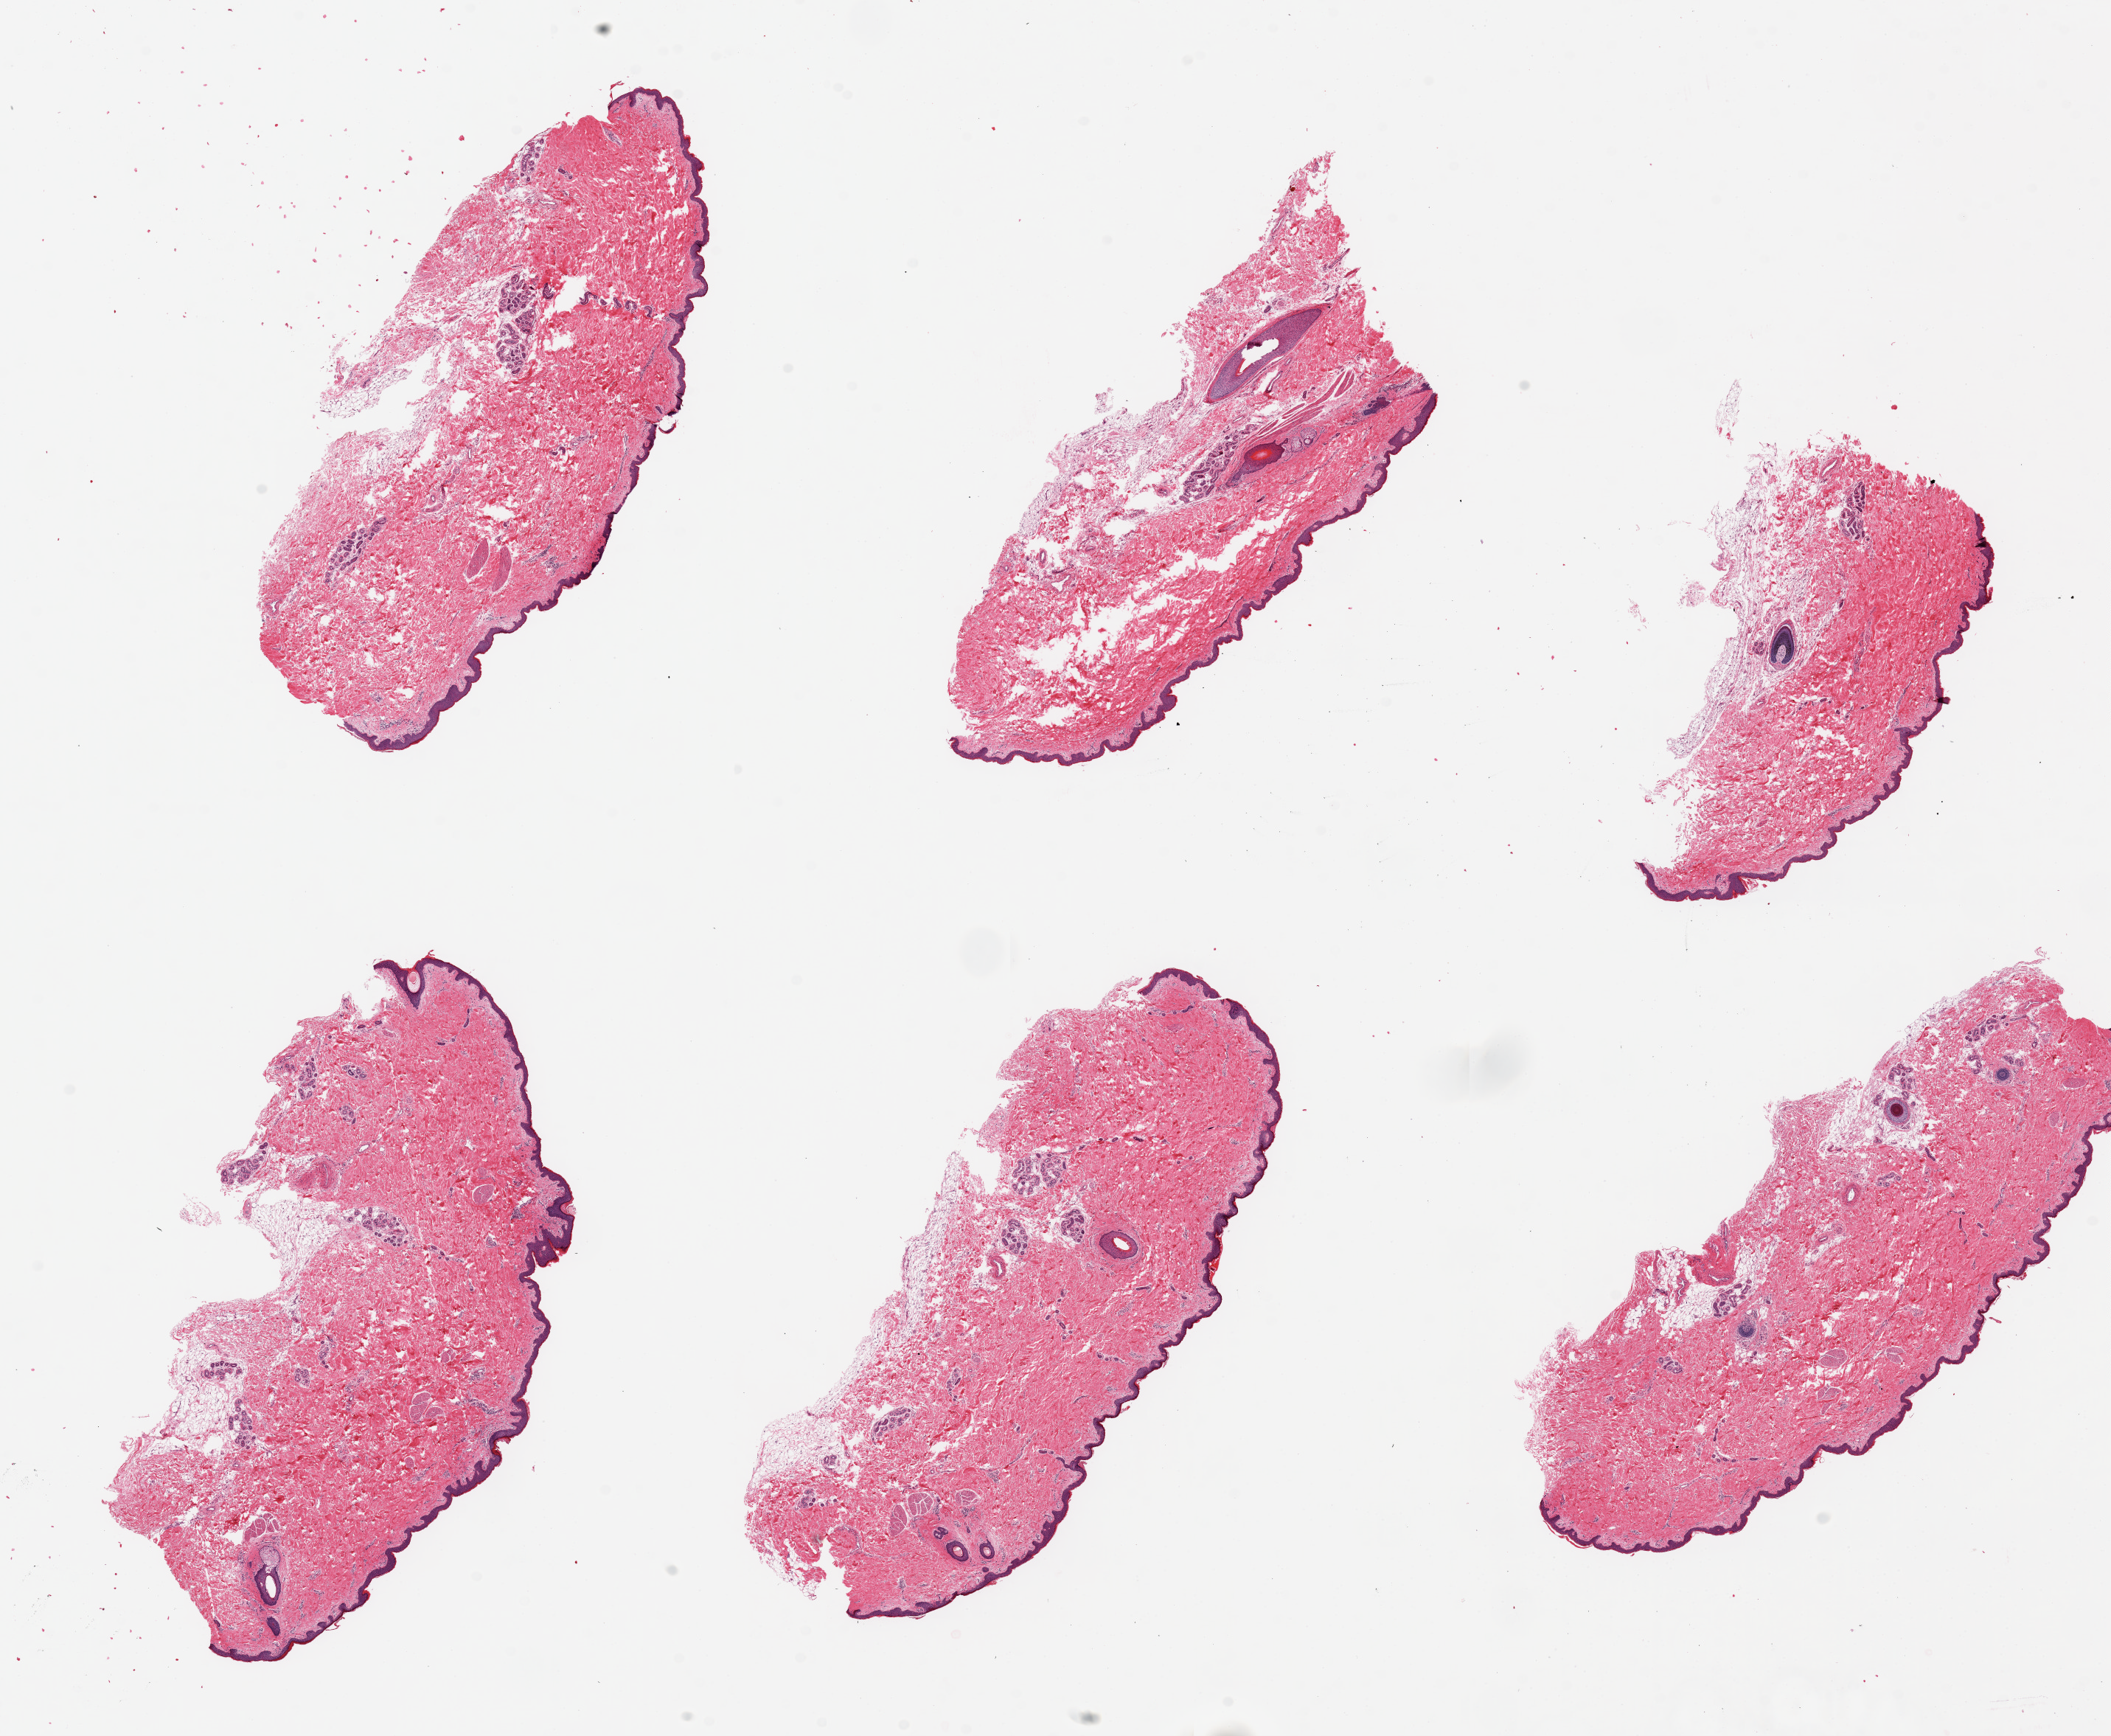
Digitized haematoxylin and eosin-stained section, a low-resolution overview of the entire scanned area, about 22.6 x 18.6 mm (slide scanned at 20x); PAXgene-fixed, paraffin-embedded tissue; section of skin of suprapubic region (target tissue); tissue donor sample. Donor sex: male.
Pathologist's review note for this sample: 6 pieces, up to 8x3mm; Subcutaneous adipose is well trimmed.